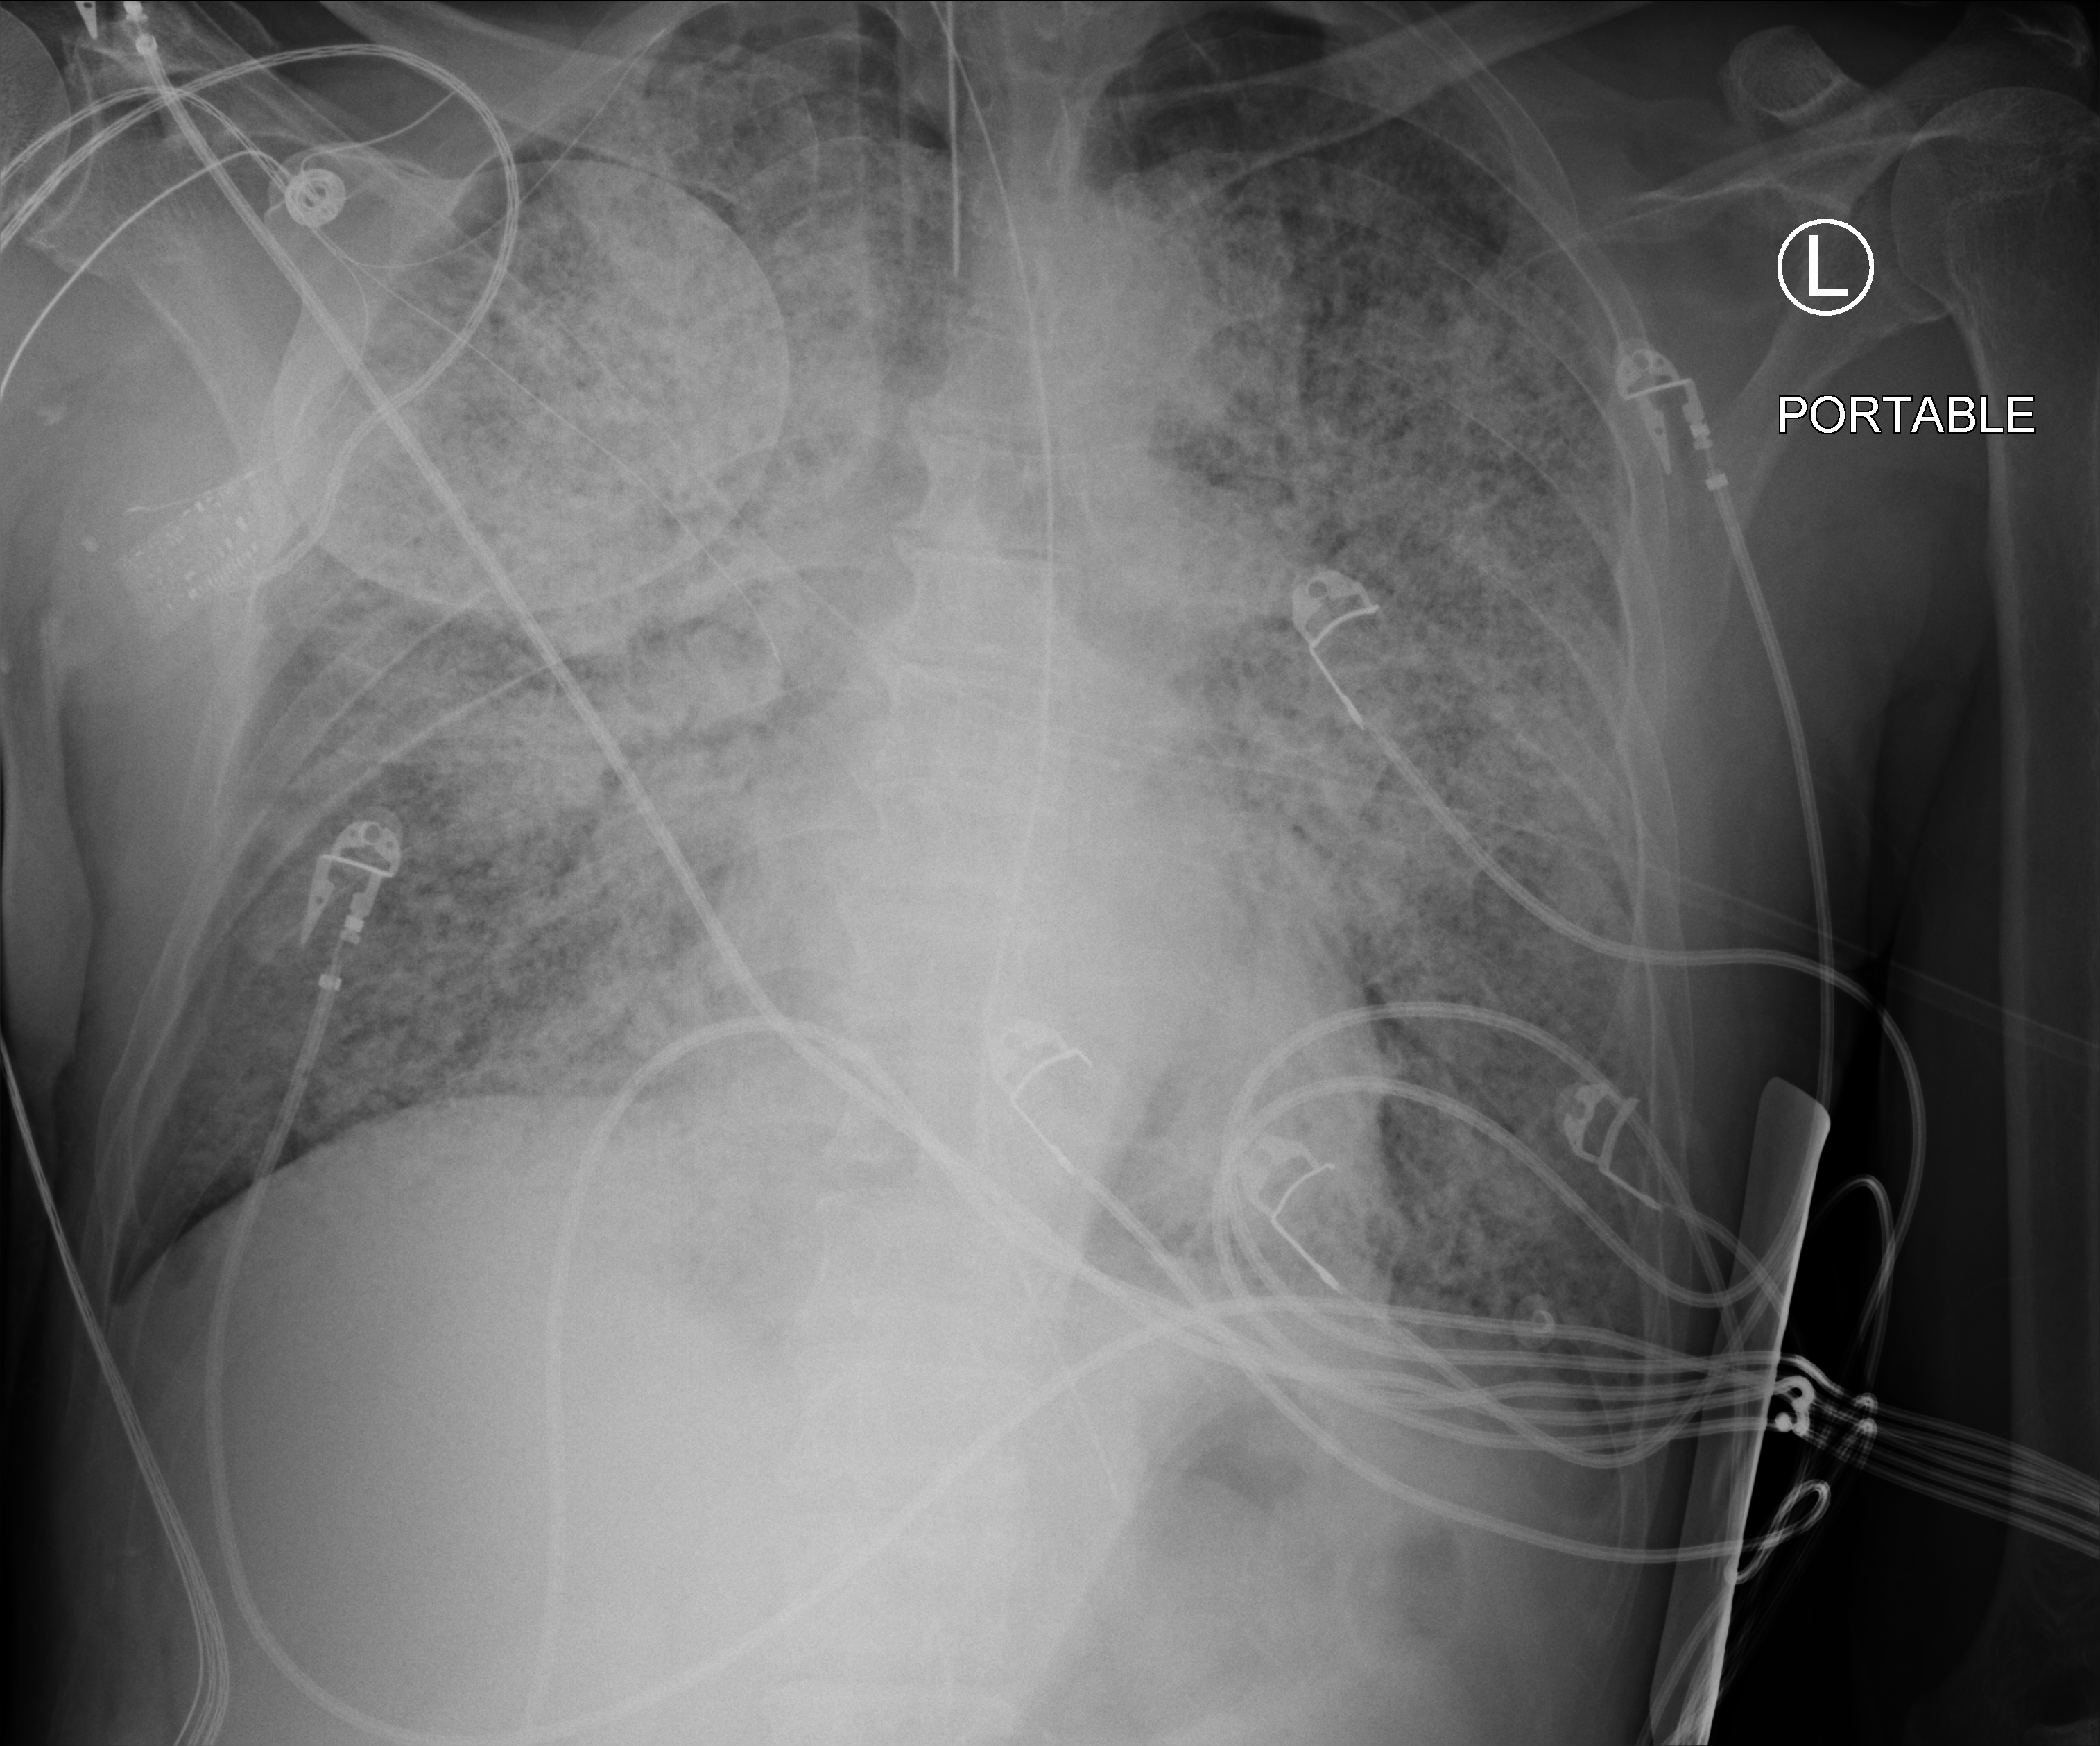
Portable chest radiograph; anteroposterior (AP) projection. Male patient hospitalised with COVID-19, age 60–74 years.
Hospital-stay facts (about this admission, not read from this image; timing relative to this image not recorded): mechanically ventilated during this hospital stay: yes.